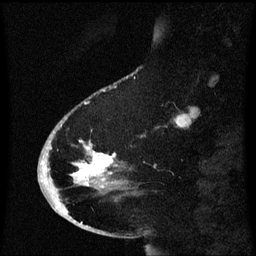
Breast MRI (dynamic contrast-enhanced), one sagittal slice. Dynamic contrast-enhanced series, image 2 of 3 at this slice position (ordered by acquisition). 1.5 T. TE 4.2 ms, TR 8.4 ms. 256 × 256 image matrix, field of view 200 × 200 mm. Patient: female, 53 years. Case-level facts recorded for this patient, not image findings: setting: breast cancer imaged before/during neoadjuvant chemotherapy; receptor status: HR-positive, HER2-negative.
Structures marked on this image (semi-automatic segmentation, software-assisted and operator-edited):
- analysis volume of interest (the breast-tissue region the enhancement analysis was run in; not a lesion): bounding box [x1, y1, x2, y2] px = [49, 112, 127, 201]
- tumour enhancement mask (voxels above the 70 % enhancement threshold inside the analysis volume of interest): [74, 148, 114, 181]